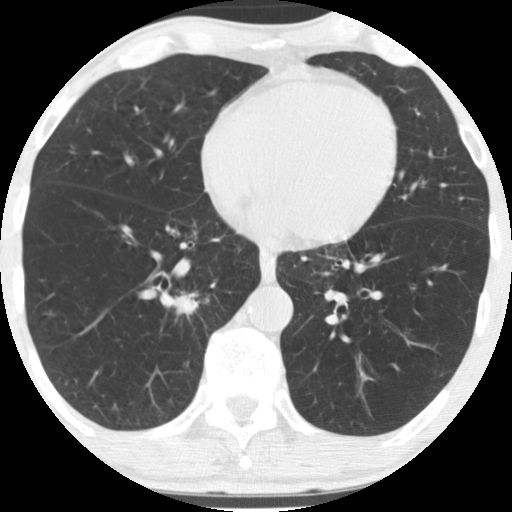
Low-dose screening chest CT, axial slice; baseline screening round; lung window (W 1500 / L -600 HU); 120 kVp; 512 × 512 image matrix, field of view 290 × 290 mm. Male, age 67 years at enrolment.
Lesion marked by an expert reader, bounding box <152,269,213,332> (left, top, right, bottom; pixels). Reader record for this screening exam (exam-level; its link to the box is not recorded): non-calcified nodule or mass ≥4 mm, right lower lobe, 16 × 16 mm, spiculated (stellate) margins, soft tissue attenuation. Participant outcome: lung cancer diagnosed 49 days after this screen — squamous cell carcinoma, NOS, right lower lobe, moderately differentiated (G2), stage IA (AJCC 6th edition), 20 mm at pathology.